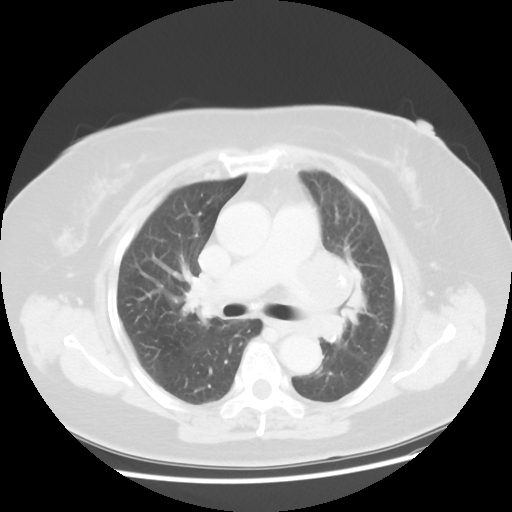
Chest CT, one axial slice; slice 28 of 49 in the series (ordered by position); reconstruction kernel STANDARD; lung window (W 1500 / L -600 HU); 512 × 512 image matrix, field of view 374 × 374 mm. Female patient, age 58 years. From the clinical record (not read from this slice): clinical TNM (as recorded): T4 N3 M0; histopathological grade: G3.
Structures marked on this image (bounding box drawn by a radiologist):
- lung tumour (recorded histology: small cell carcinoma): box from (x=289, y=245) to (x=376, y=346) px